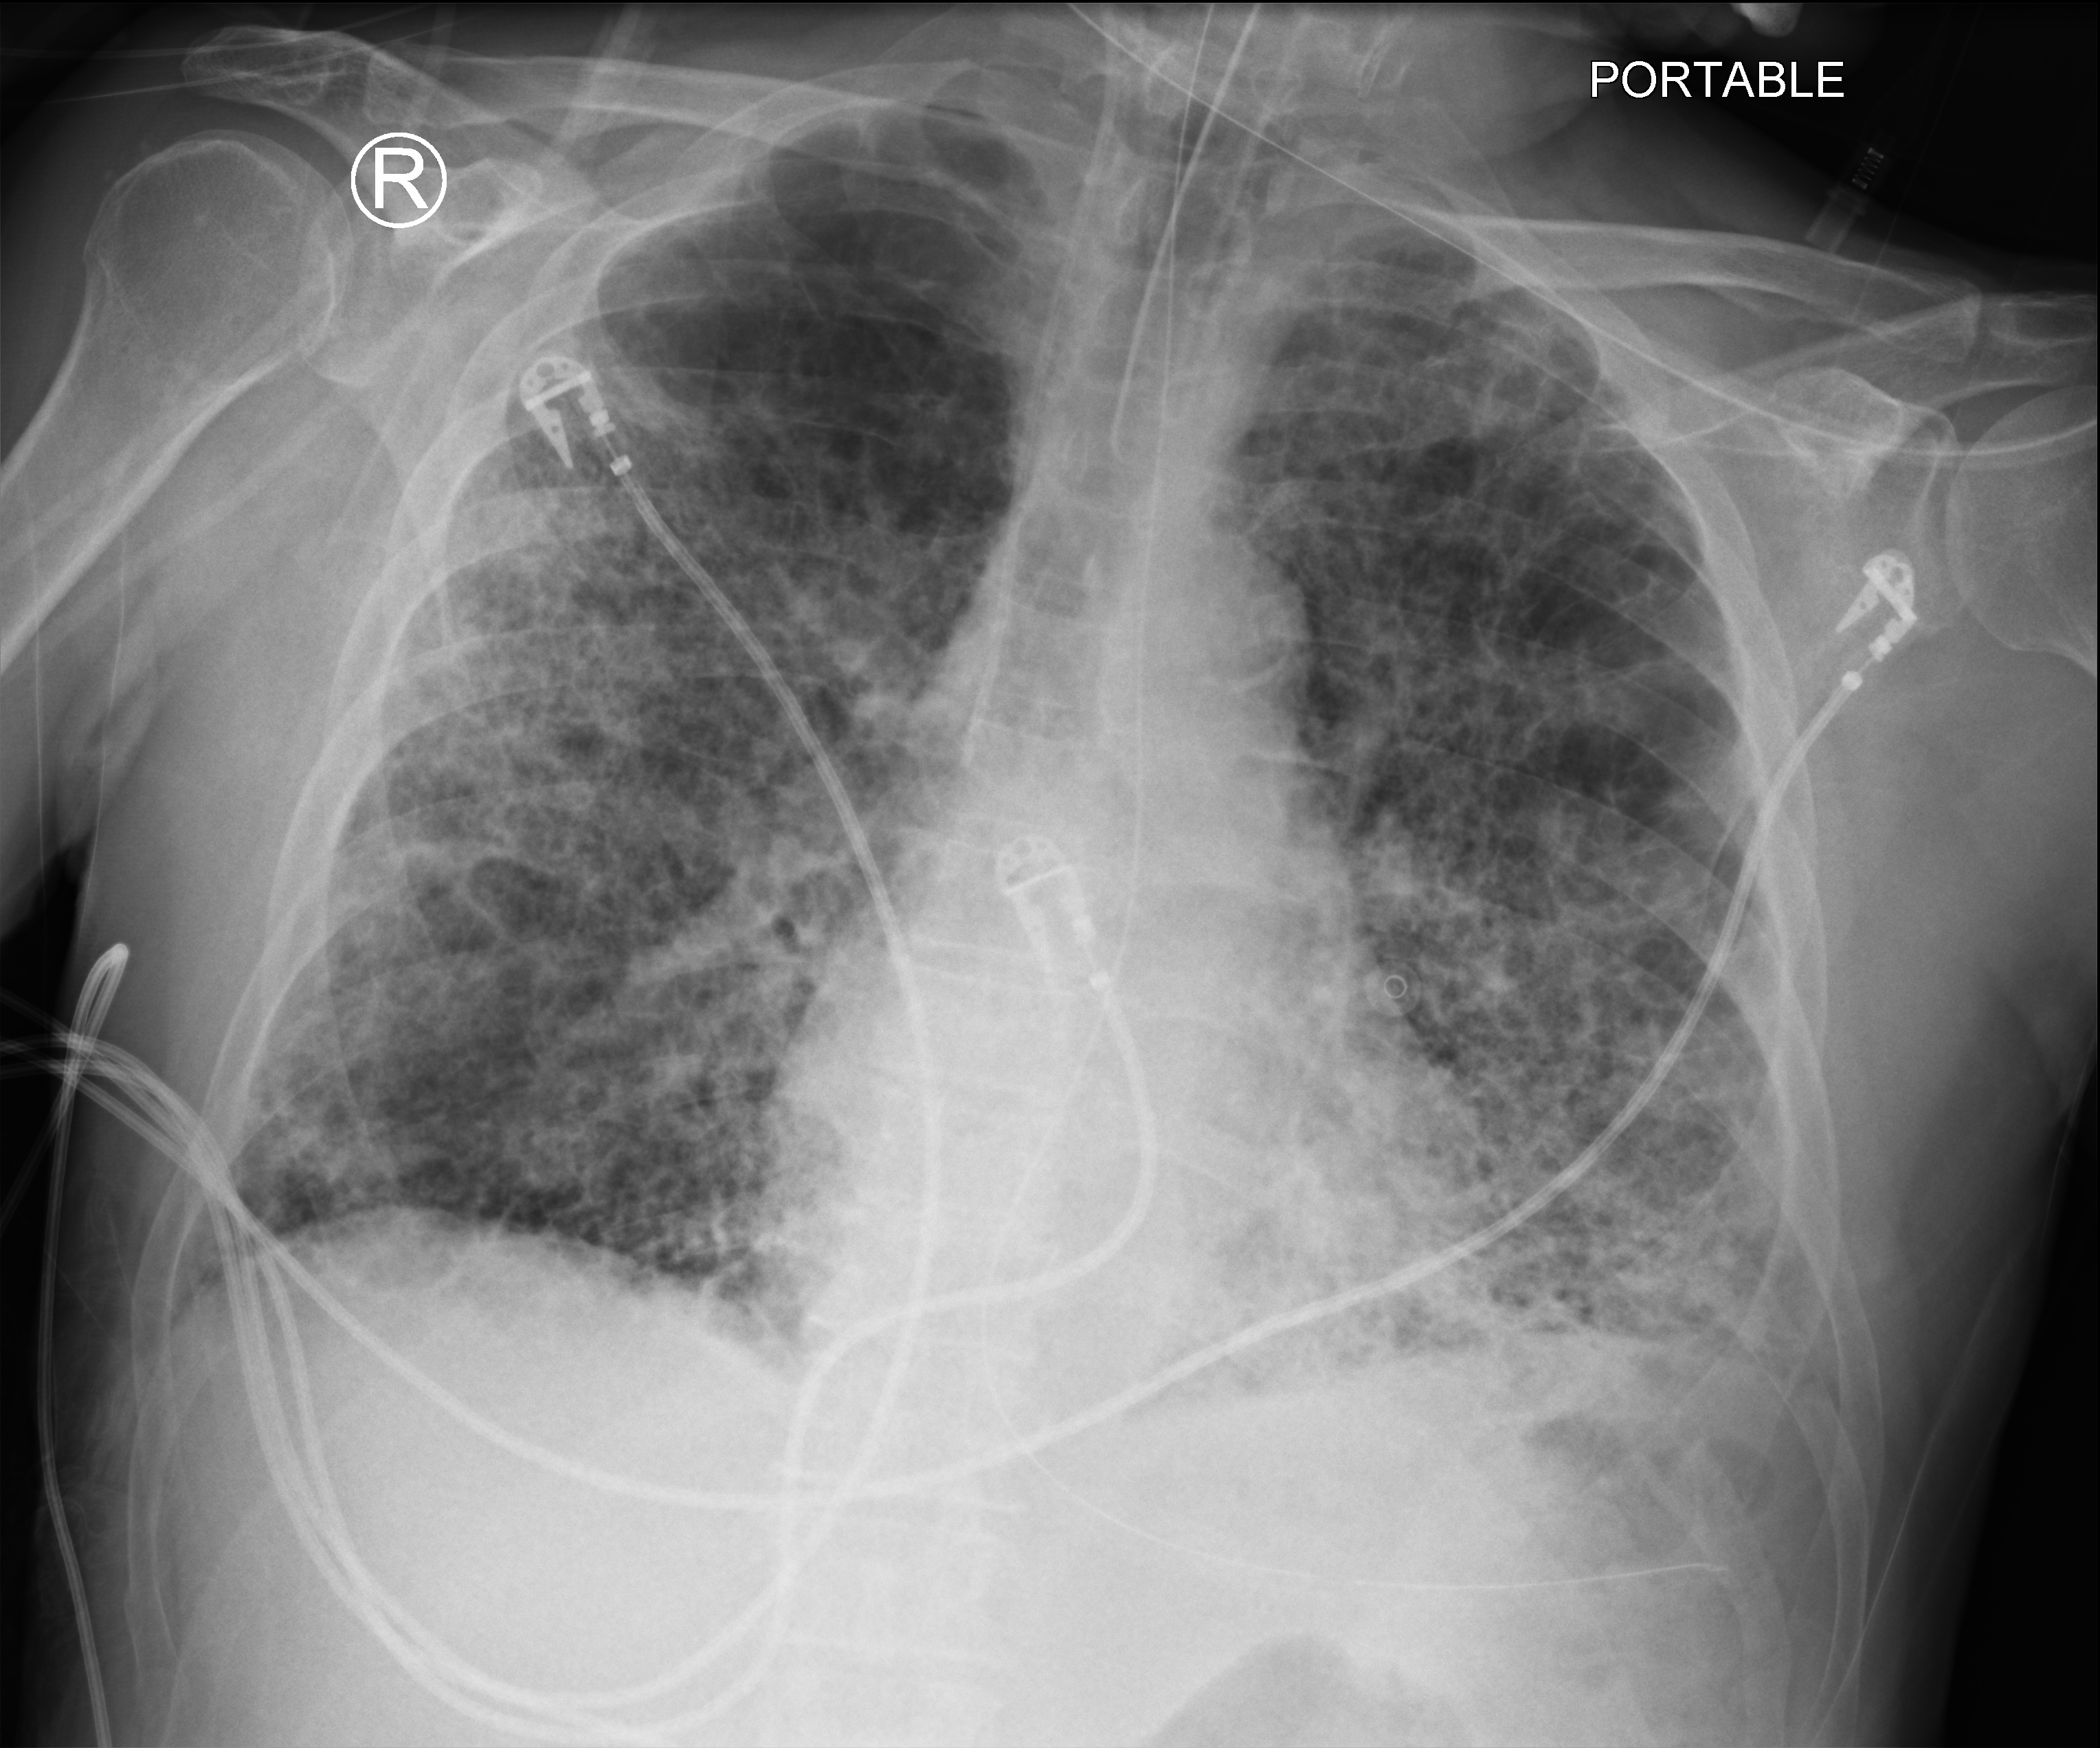
Bedside chest radiograph (computed radiography); anteroposterior (AP) projection. Patient hospitalised with COVID-19; male, aged 75–90 years.
Admission-level facts for this patient (not findings on this image; timing relative to this image not recorded): mechanically ventilated during this hospital stay: yes; admitted to intensive care during this hospital stay: yes.